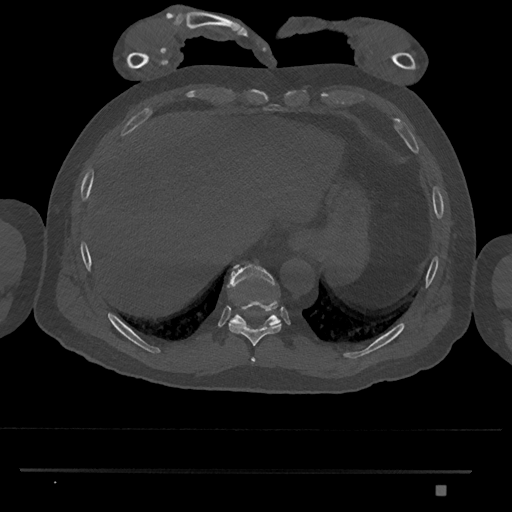
CT including the spine, one axial slice. Position 1037 of 1134 along the scan axis. Bone window (W 1800 / L 400 HU). 512 × 512 image matrix, field of view 429 × 429 mm. Patient: male, 65 years. Case-level facts recorded for this patient, not image findings: primary cancer: prostate.
Annotated regions visible in this slice (semi-automatic segmentation, software-assisted and operator-edited):
- T10 vertebra: bounding box (x1, y1, x2, y2) in pixels: (227, 264, 281, 327)
- T8 vertebra: (251, 357, 256, 363)
- T9 vertebra: (228, 299, 282, 346)